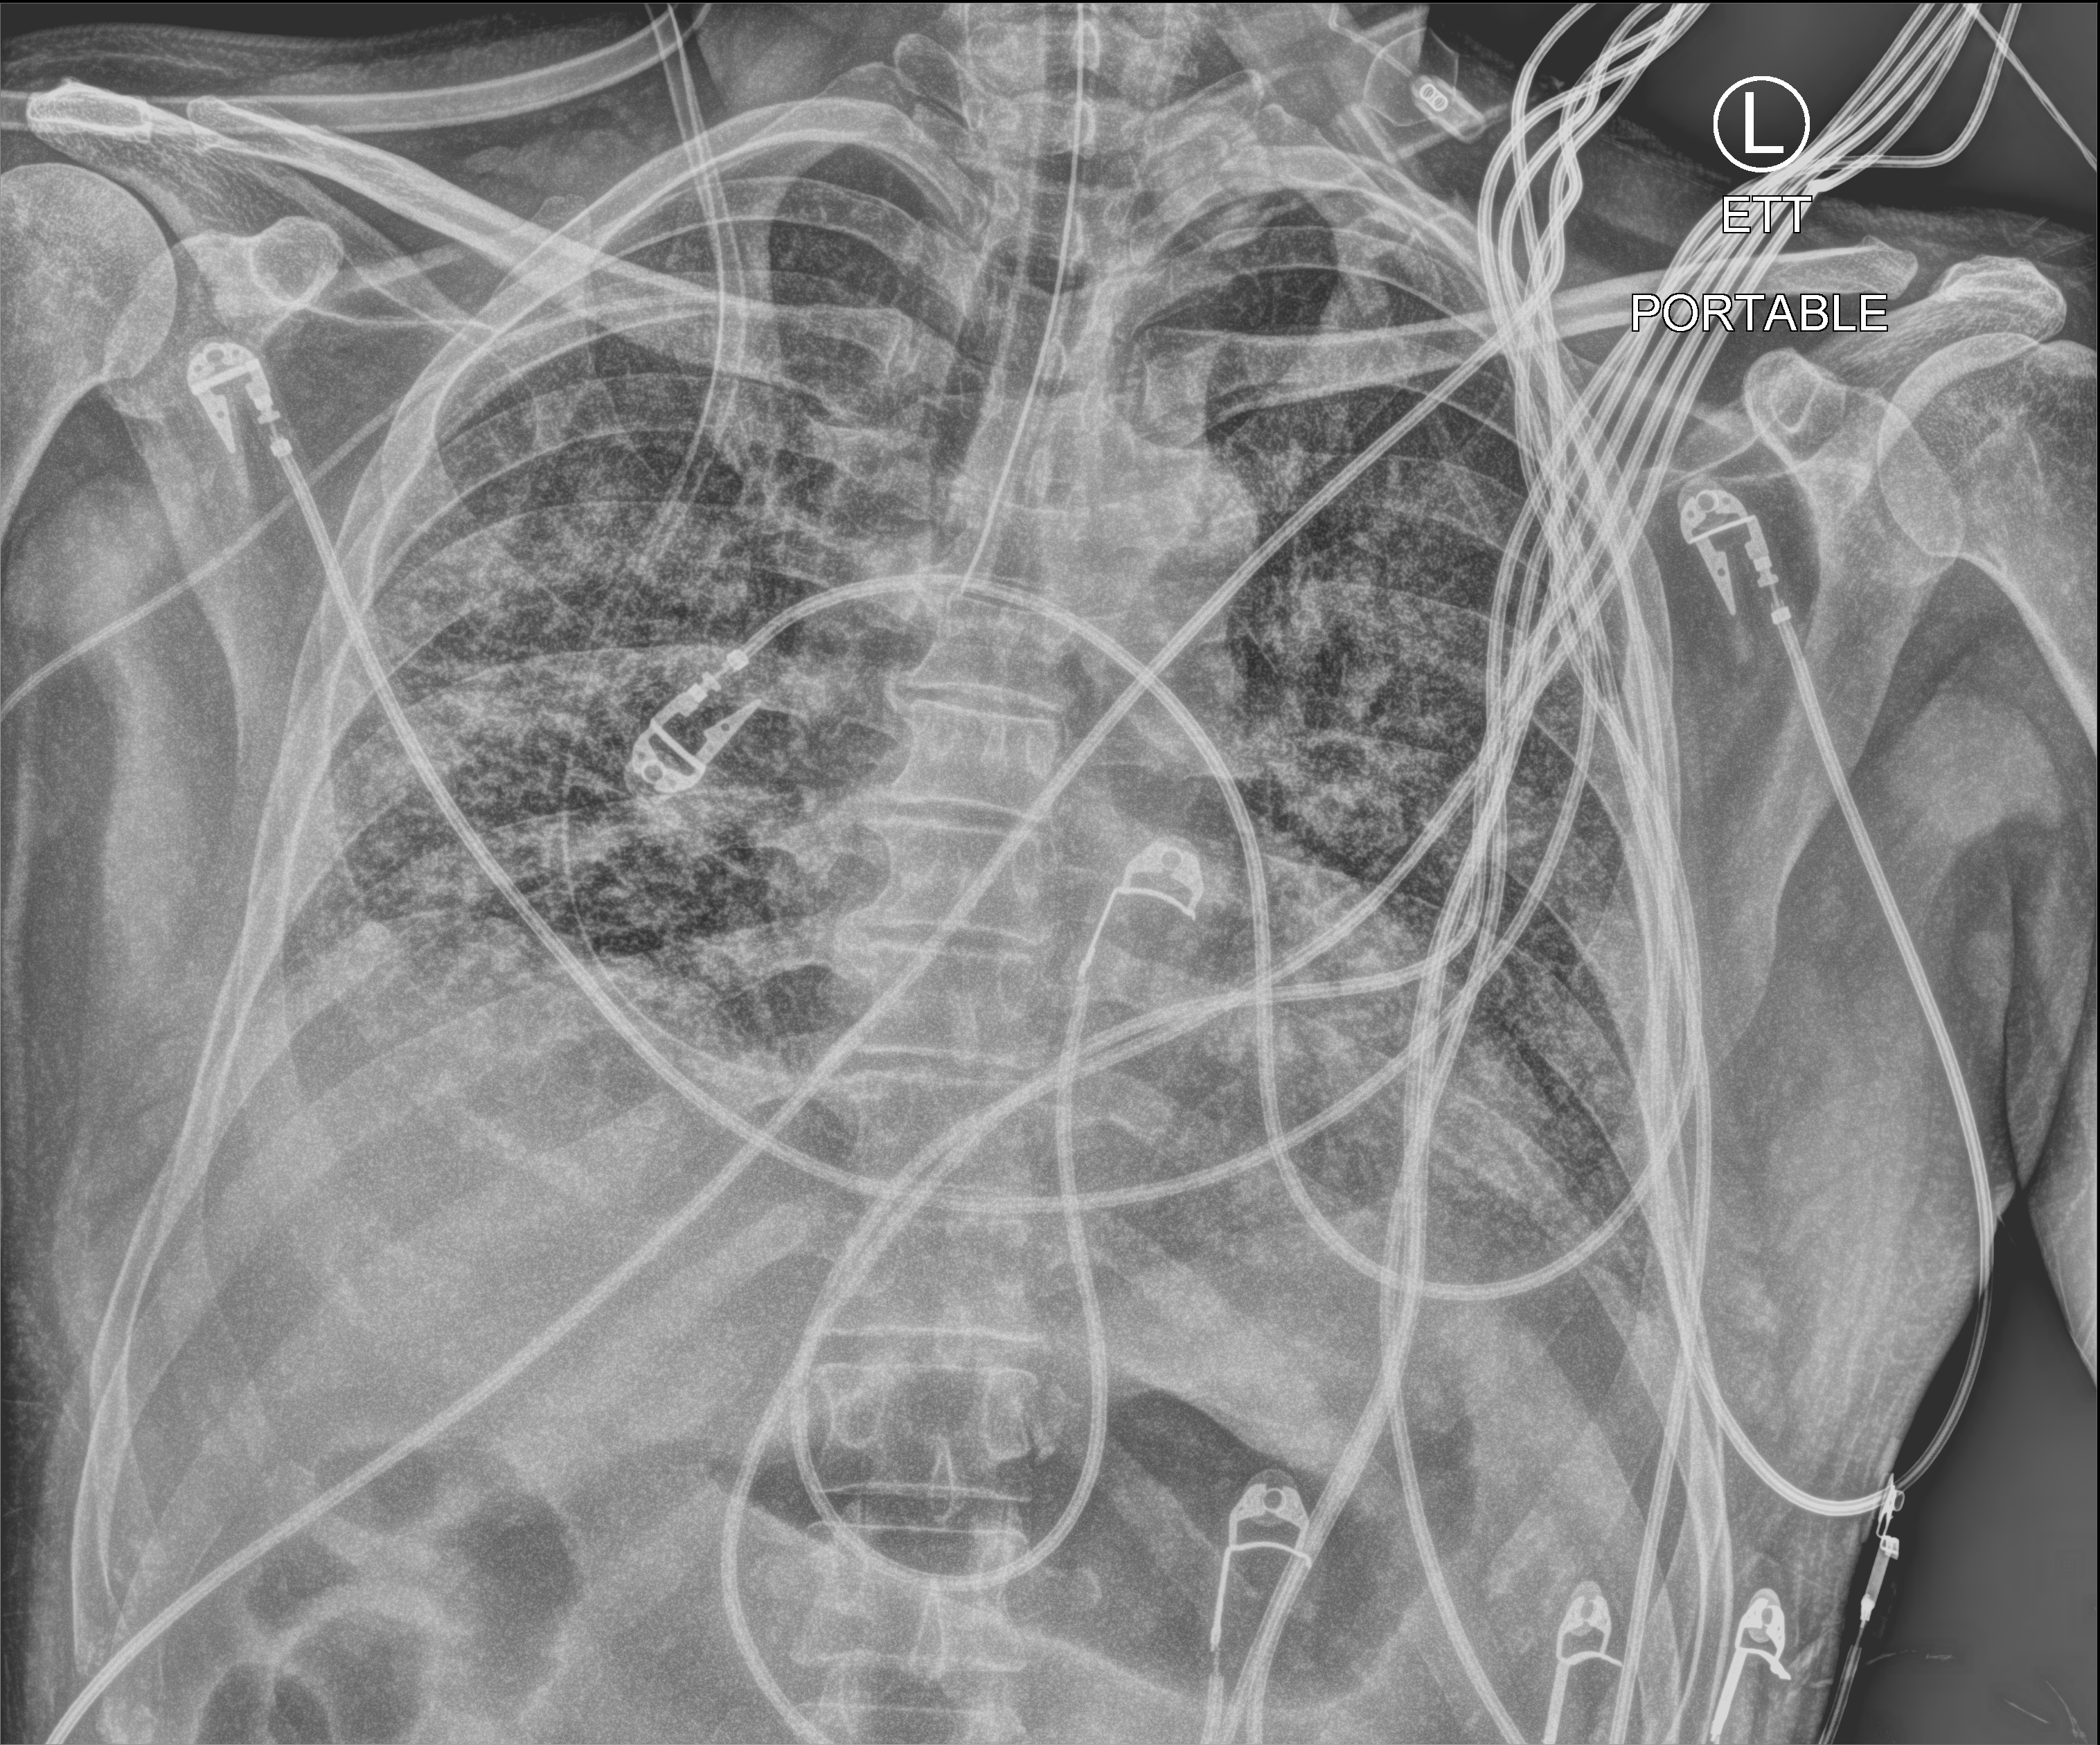
Portable chest radiograph; anteroposterior (AP) projection. Male patient hospitalised with COVID-19, age 18–59 years.
From the hospital-stay record, not from the radiograph (when in the stay this image was taken is not recorded):
- COPD (admission record): no
- smoking status (admission record): never
- length of hospital stay: 42 days